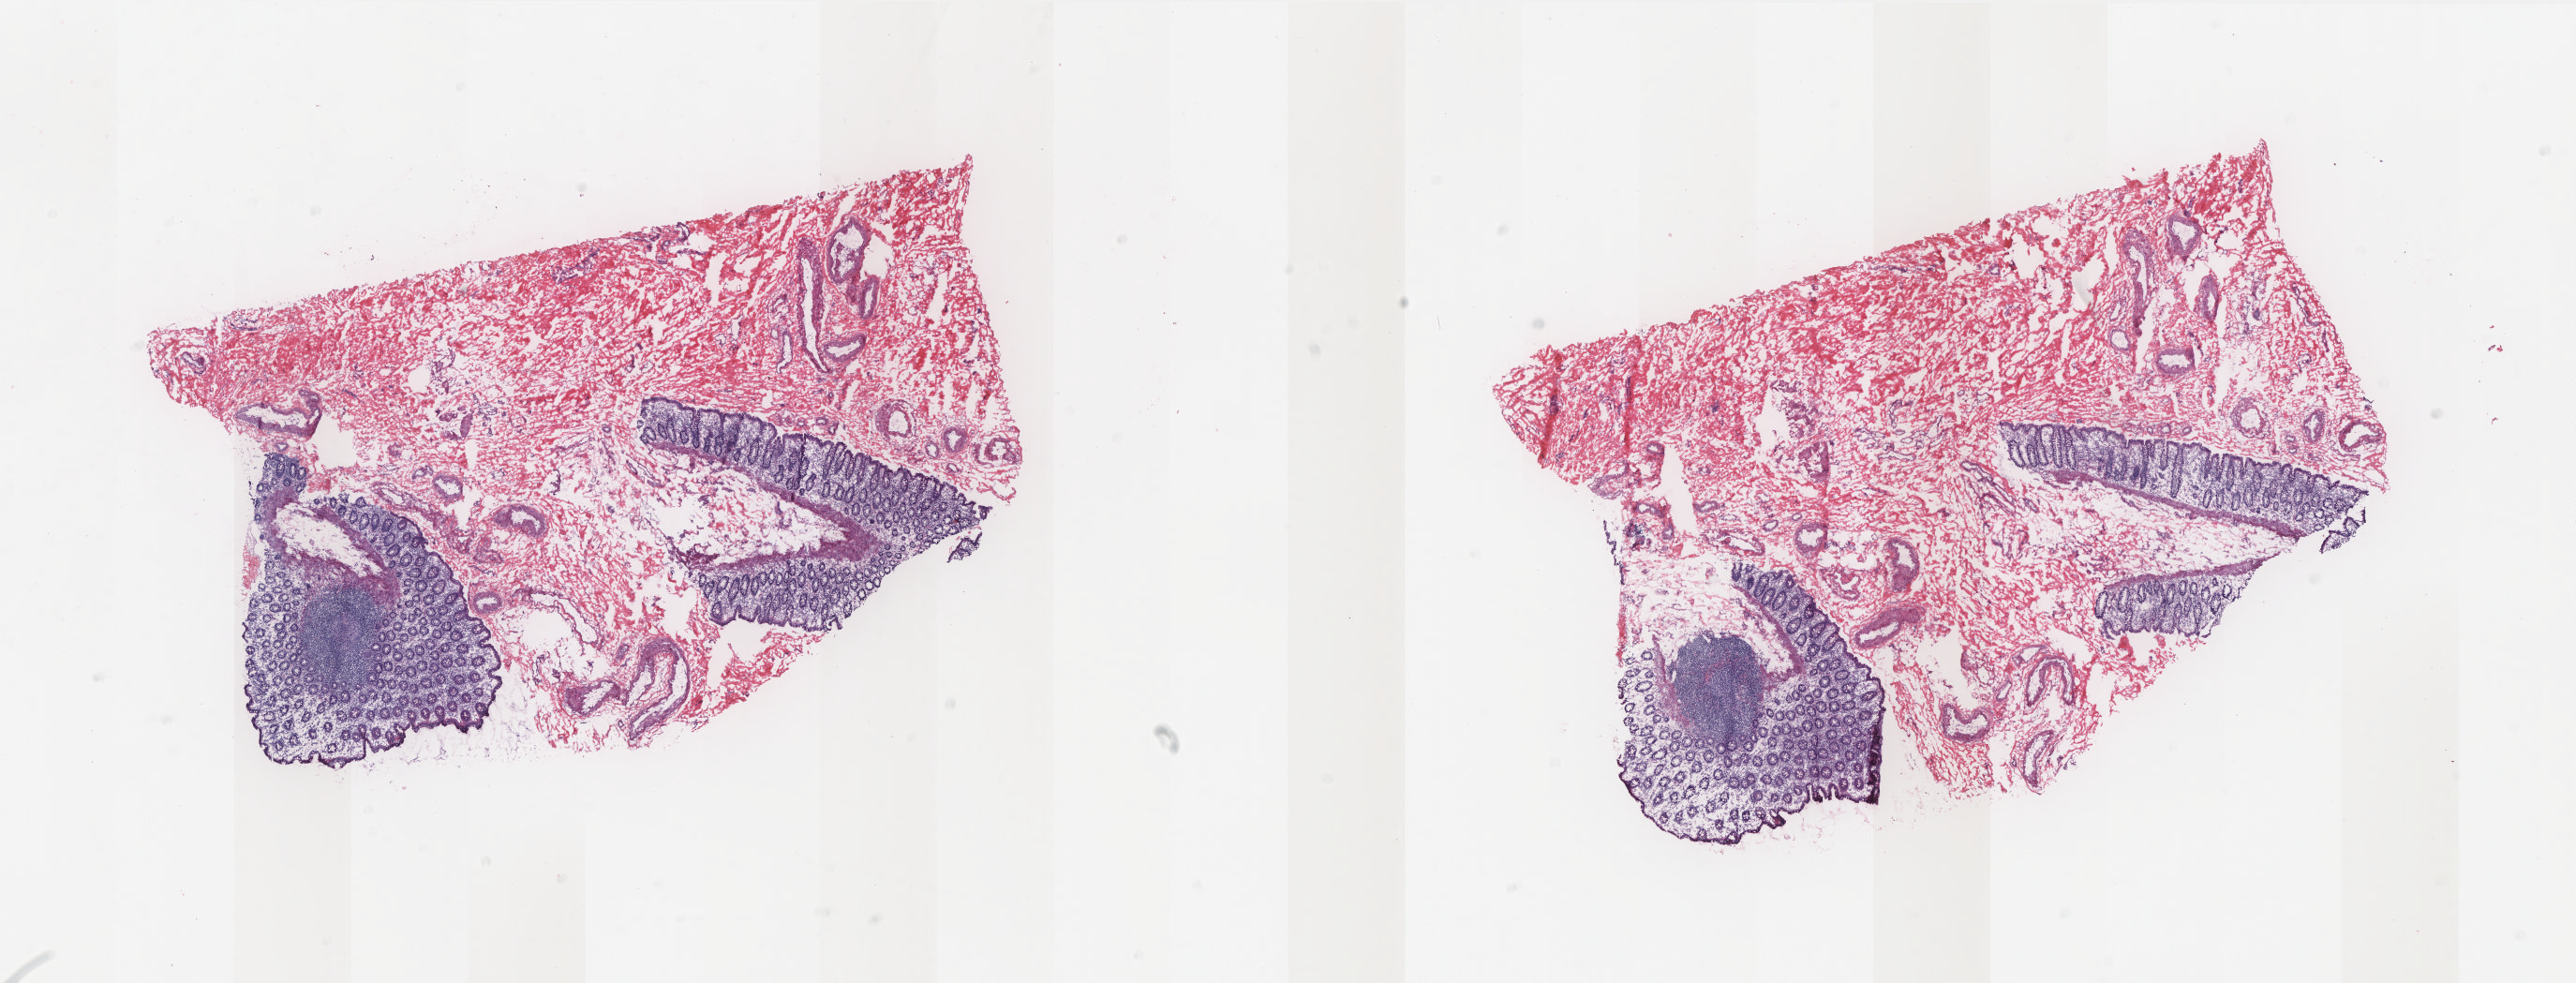
Digitized Hematoxylin and eosin (H&E) stained tissue section (whole slide), a low-resolution overview of the entire scanned area, about 22.0 x 8.4 mm, frozen section from the bottom of the tissue portion, solid tissue normal (non-tumour tissue) sample from the colon. Female, age 88 years at initial diagnosis. Slide review estimates, as recorded: tumour cells 0%, normal cells 100%. Inflammatory infiltration, as recorded: lymphocyte infiltration 50%, monocyte infiltration 10%, neutrophil infiltration 0%.
* this section: solid tissue normal (non-tumour) sample from the same patient
* patient diagnosis: Adenocarcinoma, NOS (cecum)